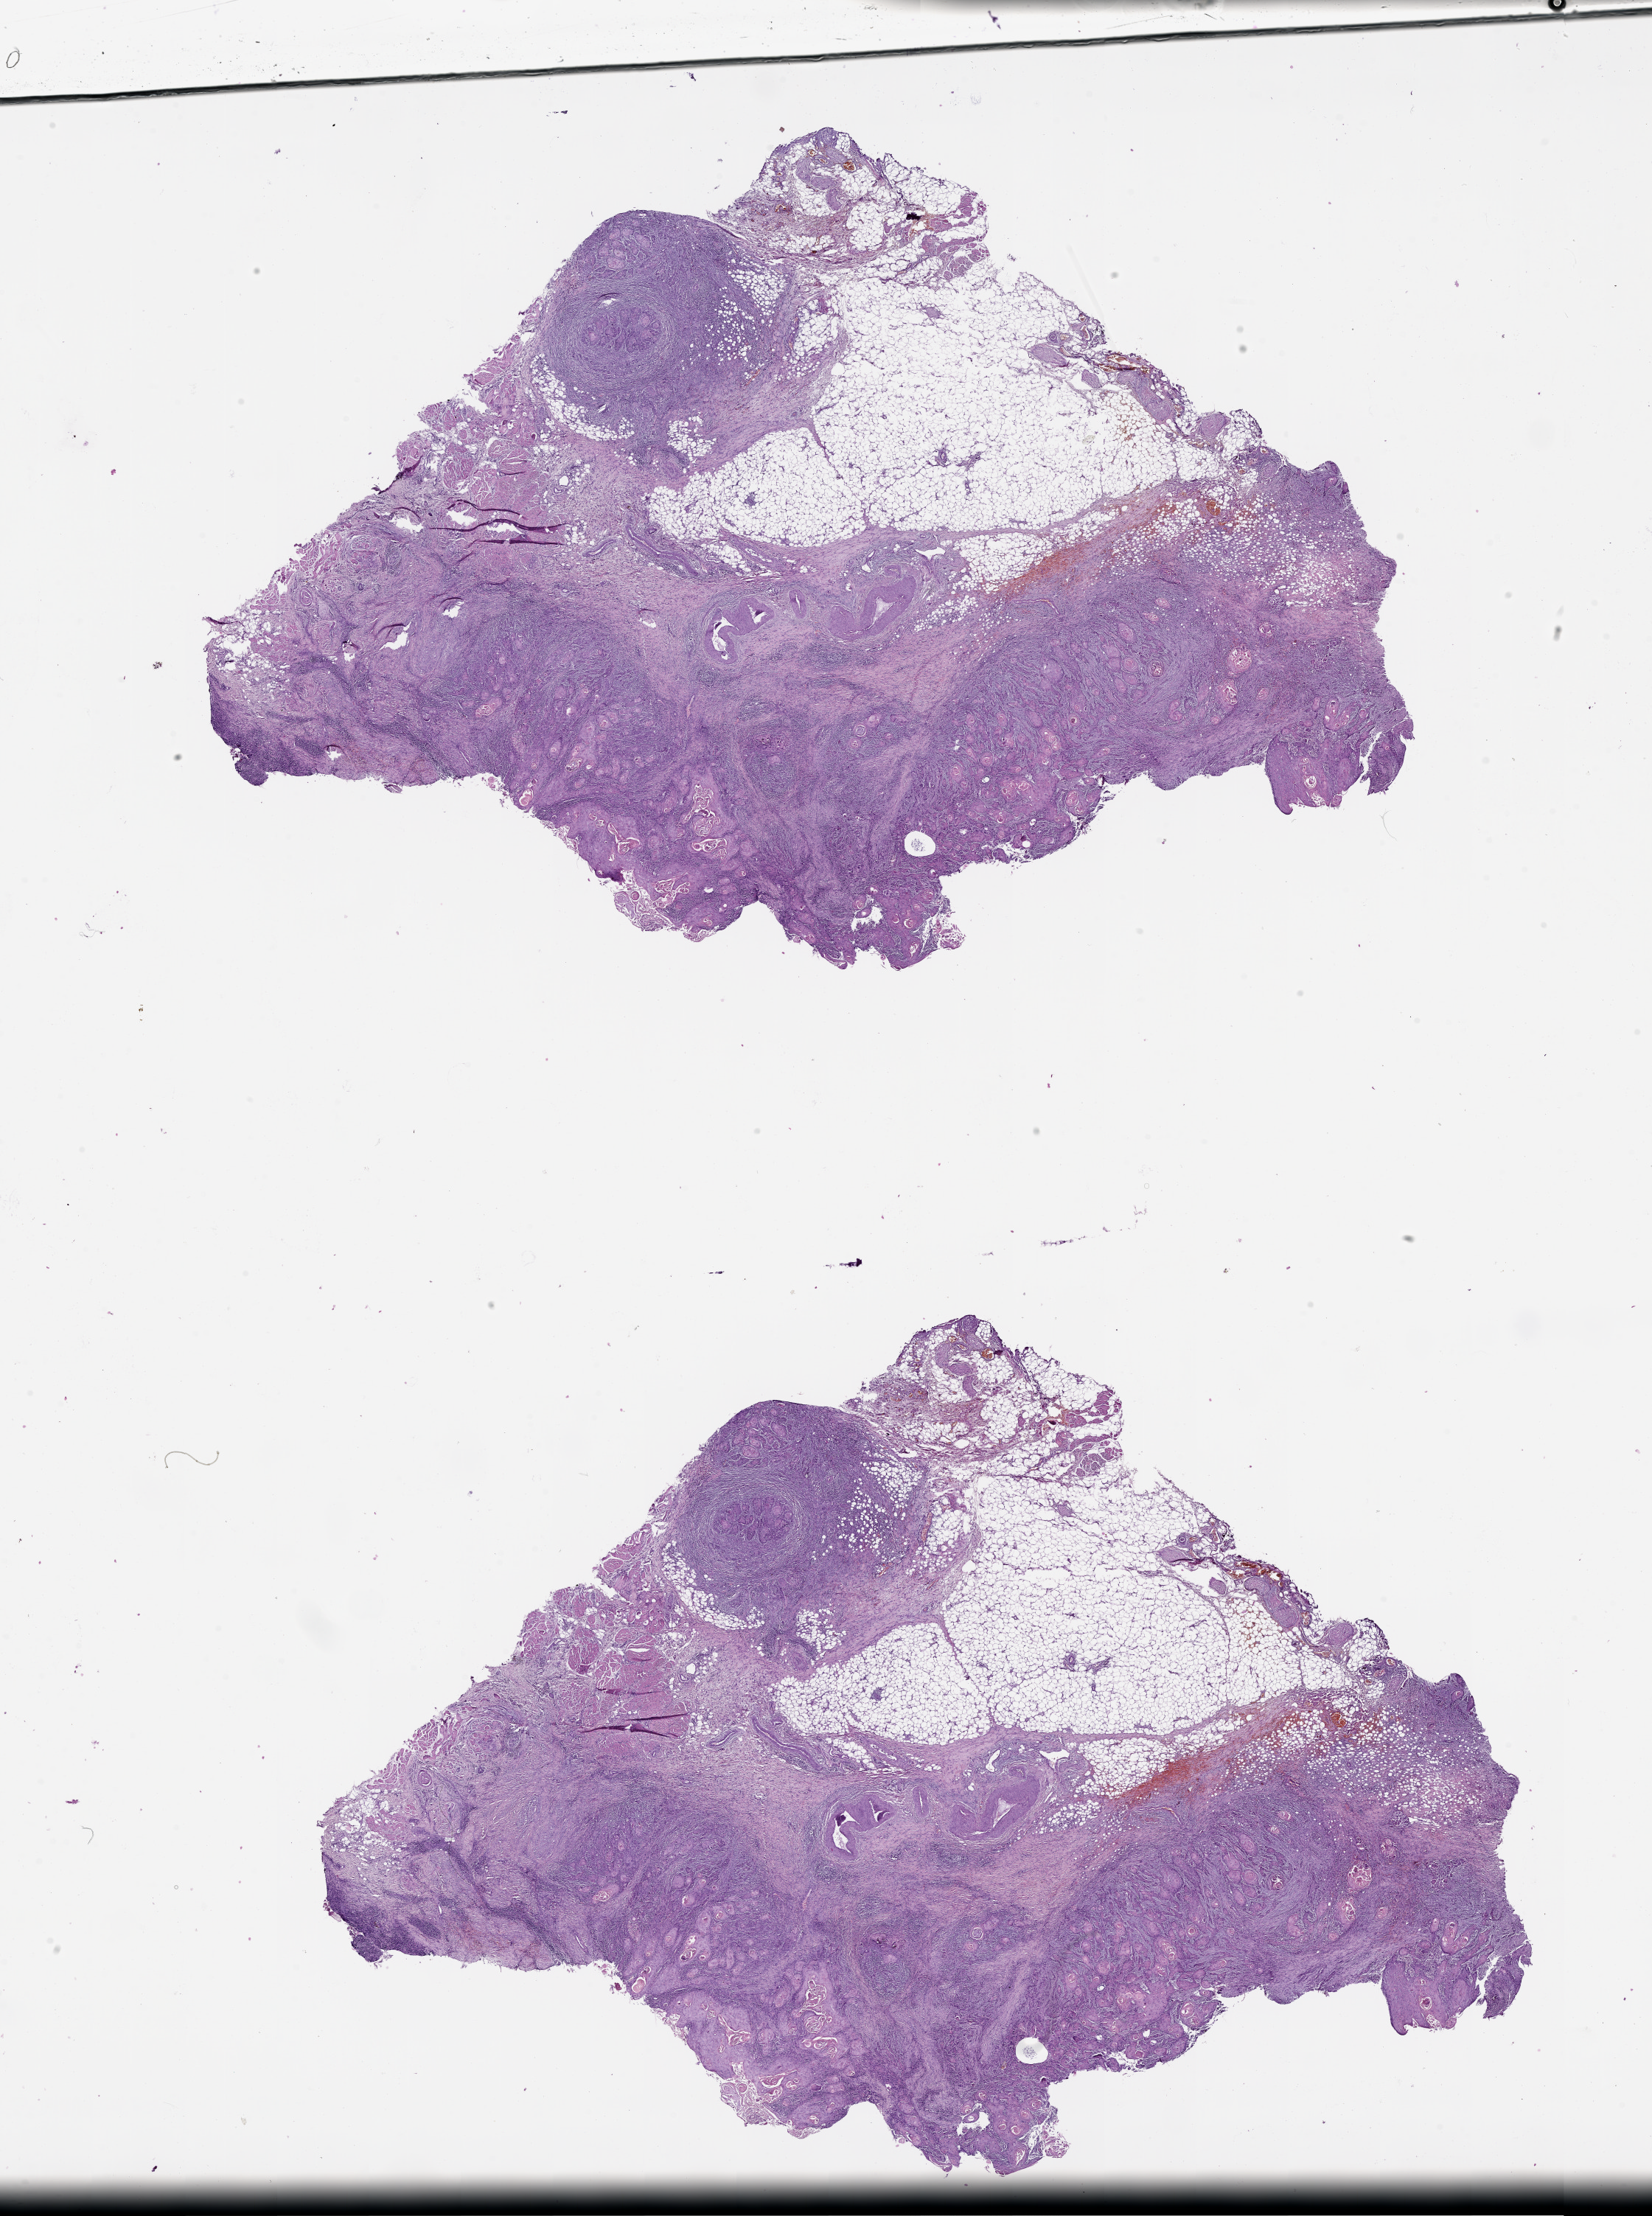
Whole-slide histology image, H&E-stained — shown as a low-resolution overview of the whole scanned area (about 18.0 x 24.2 mm, acquisition: 20x scan); head and neck, tissue type not recorded.
Patient diagnosis (cohort enrolment): head and neck cancer (head-neck).